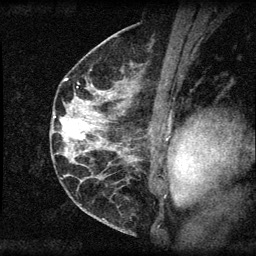
Breast MRI (dynamic contrast-enhanced), one sagittal slice; dynamic contrast-enhanced series, image 2 of 3 at this slice position (ordered by acquisition); 1.5 T; TE 4.2 ms, TR 8.2 ms; 2 mm slice thickness; 256 × 256 image matrix, field of view 180 × 180 mm. Female patient, age 45 years.
Annotated regions visible in this slice (semi-automatic segmentation, software-assisted and operator-edited):
- analysis volume of interest (the breast-tissue region the enhancement analysis was run in; not a lesion): box from (x=55, y=110) to (x=94, y=148) px
- tumour enhancement mask (voxels above the 70 % enhancement threshold inside the analysis volume of interest): (x=55, y=117)–(x=86, y=140)